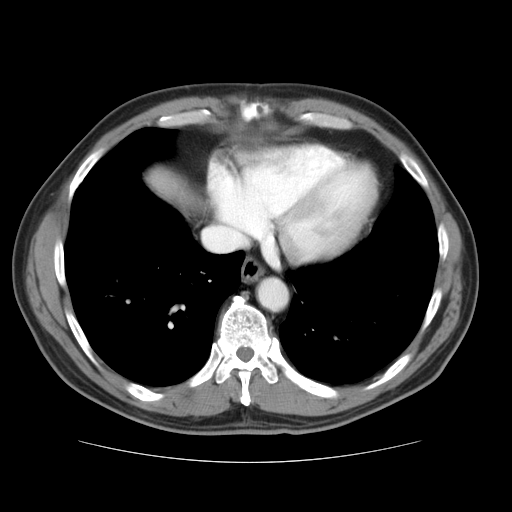
Contrast-enhanced abdominal CT, one axial slice. Slice 35 of 37 in the series (ordered by position). Reconstruction kernel STANDARD. 120 kVp. Intravenous contrast given. Soft-tissue window (W 400 / L 40 HU). 5 mm slice thickness. 512 × 512 image matrix, field of view 374 × 374 mm. Male patient, age 66 years. Case-level facts recorded for this patient, not image findings: diagnosis: colorectal cancer liver metastases, imaged before liver resection; multiple liver metastases: yes; largest metastasis: 1.6 cm; chemotherapy before resection: no.
Outlined on this slice (manually delineated by an expert):
- liver: box from (x=145, y=168) to (x=208, y=216) px
- planned liver remnant (the part of the liver to remain after resection): (x=155, y=181)–(x=208, y=216)